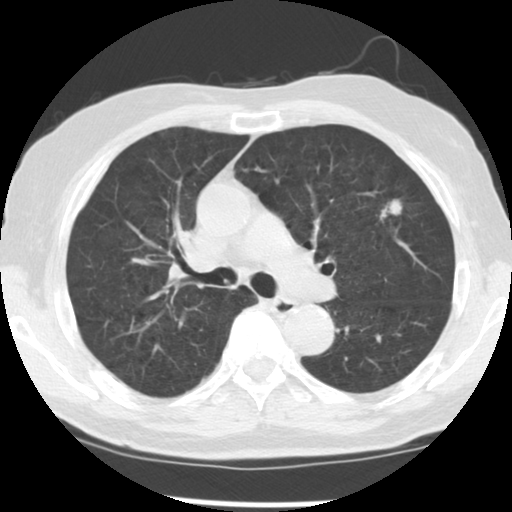
Chest CT (low-dose screening protocol), one axial image, third screening round (two years after baseline), lung window (W 1500 / L -600 HU), 2.5 mm slice thickness, 512 × 512 image matrix, field of view 330 × 330 mm. Male participant, aged 70 years at enrolment.
Expert-annotated lung lesion, box from (x=356, y=184) to (x=414, y=243) px. The screening reader recorded 3 non-calcified nodules or masses ≥4 mm on this exam; which of them this box marks is not recorded. Lung cancer was diagnosed 74 days after this screen: adenocarcinoma, NOS, left upper lobe, moderately differentiated (G2), stage IIIA (AJCC 6th edition), 17 mm at pathology.